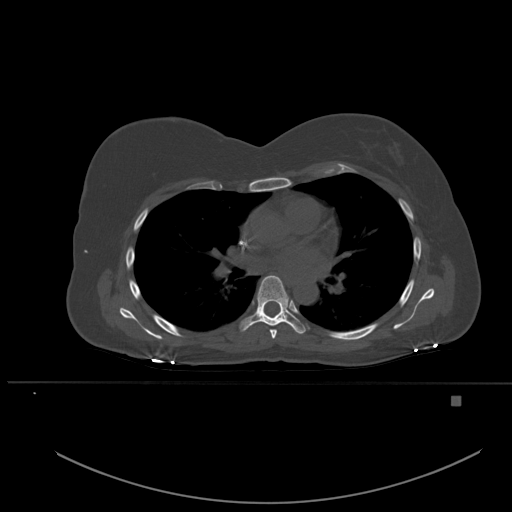
CT including the spine, one axial slice; bone window (W 1800 / L 400 HU); 512 × 512 image matrix. Patient: female, 49 years. Case-level facts recorded for this patient, not image findings: primary cancer: breast.
Structures marked on this image (semi-automatically segmented with operator editing):
- T5 vertebra: bounding box [x1, y1, x2, y2] px = [270, 329, 277, 339]
- T6 vertebra: [240, 275, 306, 334]